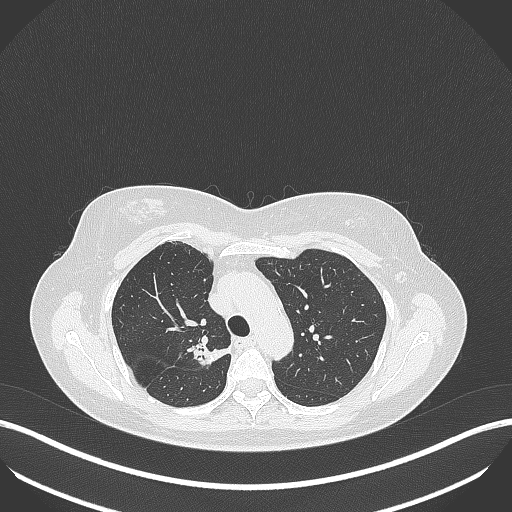
Chest CT, one axial slice. Slice 285 of 386 in the series (ordered by position). Reconstruction kernel B70f. Lung window (W 1500 / L -600 HU). 1 mm slice thickness. 512 × 512 image matrix, field of view 400 × 400 mm. Female patient, age 65 years. From the clinical record (not read from this slice): clinical TNM (as recorded): T1b N0 M0; histopathological grade: G2.
Structures marked on this image (bounding box drawn by a radiologist):
- lung tumour (recorded histology: adenocarcinoma): bounding box [x1, y1, x2, y2] px = [189, 339, 230, 368]